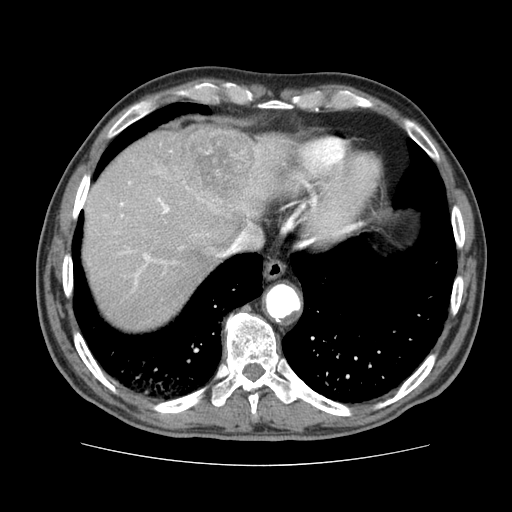
Contrast-enhanced abdominal CT (liver protocol), one axial slice. Position 66 of 79 along the scan axis. Reconstruction kernel STANDARD. 120 kVp. Soft-tissue window (W 400 / L 40 HU). 512 × 512 image matrix. Case-level facts recorded for this patient, not image findings: diagnosis: hepatocellular carcinoma (patient treated with transarterial chemoembolisation; whether this scan precedes or follows treatment is not stated here); TNM stage (as recorded): Stage-I.
Structures marked on this image (semi-automatically segmented with operator editing):
- liver parenchyma outside the tumour (the mass and vessels are separate outlines, so this box may not span the whole liver): bounding box (x1, y1, x2, y2) in pixels: (82, 126, 292, 328)
- mass: (145, 127, 290, 220)
- liver vessels: (121, 182, 170, 285)